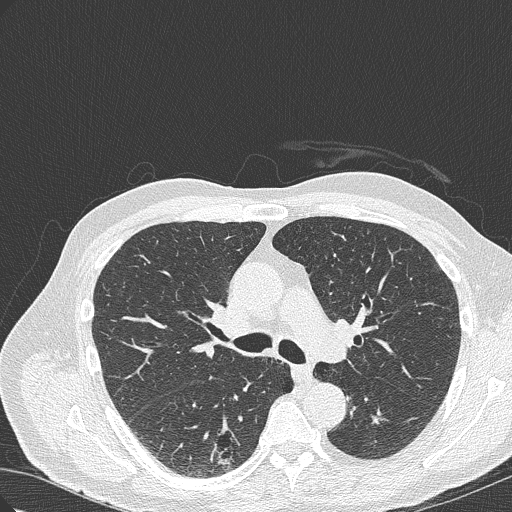
Low-dose screening chest CT, axial slice; baseline screening round; lung window (W 1500 / L -600 HU); lung (sharp) reconstruction kernel (B50f); slice 118 of 322 in the series; 512 × 512 image matrix, field of view 350 × 350 mm. Male participant, aged 70 years at enrolment. Current smoker at enrolment.
Expert reader's lesion annotation, box from (x=200, y=419) to (x=264, y=469) px. The screening reader recorded 4 non-calcified nodules or masses ≥4 mm on this exam; which of them this box marks is not recorded. Official screen result: positive, change unspecified: nodule(s) >= 4 mm or enlarging nodule(s), mass(es), or other non-specific abnormalities suspicious for lung cancer. Lung cancer was diagnosed 978 days after this screen (after the third annual screen): bronchiolo-alveolar adenocarcinoma, NOS, right lower lobe, poorly differentiated (G3), stage IB (AJCC 6th edition), 30 mm at pathology.